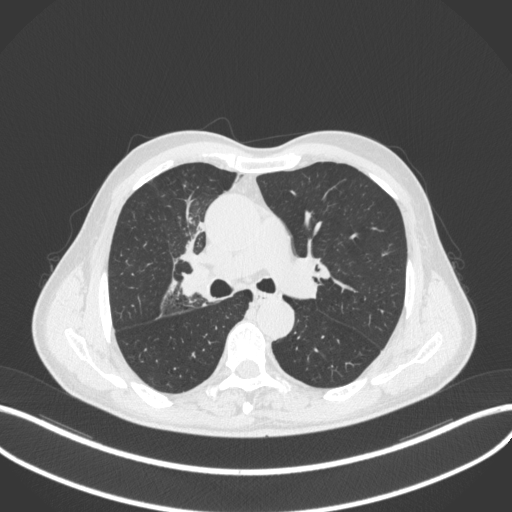
Chest CT, one axial slice; position 302 of 490 along the scan axis; reconstruction kernel B31f; 120 kVp; lung window (W 1500 / L -600 HU); 1 mm slice thickness; 512 × 512 image matrix, field of view 400 × 400 mm. Patient: male, 69 years. From the clinical record (not read from this slice): clinical TNM (as recorded): T2a N0 M0.
Annotated regions visible in this slice (rectangle marked by the reading radiologist):
- lung tumour (recorded histology: adenocarcinoma): bounding box (x1, y1, x2, y2) in pixels: (176, 264, 212, 303)